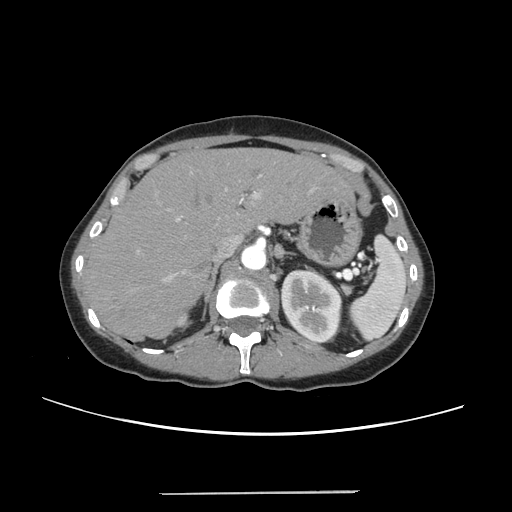
Contrast-enhanced abdominal CT, one axial slice. Slice 169 of 240 in the series (ordered by position). 120 kVp. Intravenous contrast given. Soft-tissue window (W 400 / L 40 HU). 1.25 mm slice thickness. 512 × 512 image matrix, field of view 371 × 371 mm. Female patient, age 60 years. Case-level facts recorded for this patient, not image findings: diagnosis: colorectal cancer liver metastases, imaged before liver resection; multiple liver metastases: no; largest metastasis: 1.5 cm; disease in both lobes: no.
Structures marked on this image (manually delineated by an expert):
- liver: bounding box (x1, y1, x2, y2) in pixels: (86, 149, 349, 337)
- planned liver remnant (the part of the liver to remain after resection): (86, 149, 348, 337)
- portal vein (with intrahepatic branches): (132, 172, 313, 291)